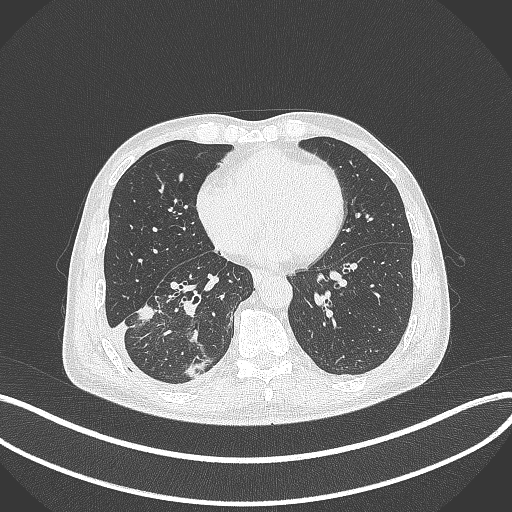
Chest CT, one axial slice. Reconstruction kernel B70f. 120 kVp. Lung window (W 1500 / L -600 HU). 1 mm slice thickness. 512 × 512 image matrix. Male patient, age 64 years. Case-level facts recorded for this patient, not image findings: clinical TNM (as recorded): T3 N0 M0.
Outlined on this slice (bounding box drawn by a radiologist):
- lung tumour (recorded histology: adenocarcinoma): bounding box <130,299,159,325> (left, top, right, bottom; pixels)